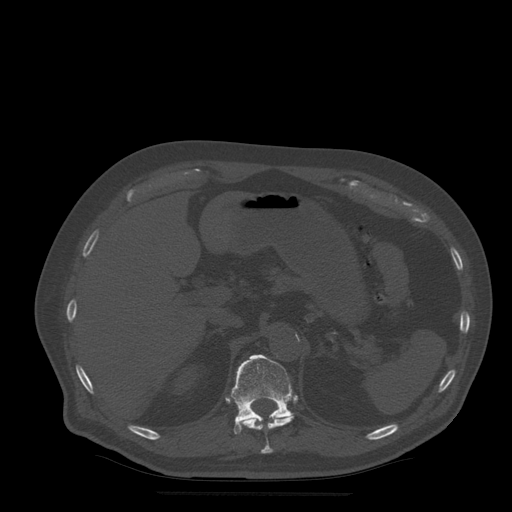
CT including the spine, one axial slice; position 230 of 522 along the scan axis; bone window (W 1800 / L 400 HU); 512 × 512 image matrix, field of view 420 × 420 mm. Patient age 72 years. From the clinical record (not read from this slice): primary cancer: prostate.
Annotated regions visible in this slice (semi-automatically segmented with operator editing):
- T11 vertebra: bounding box [x1, y1, x2, y2] px = [235, 414, 294, 454]
- T12 vertebra: [231, 355, 294, 434]